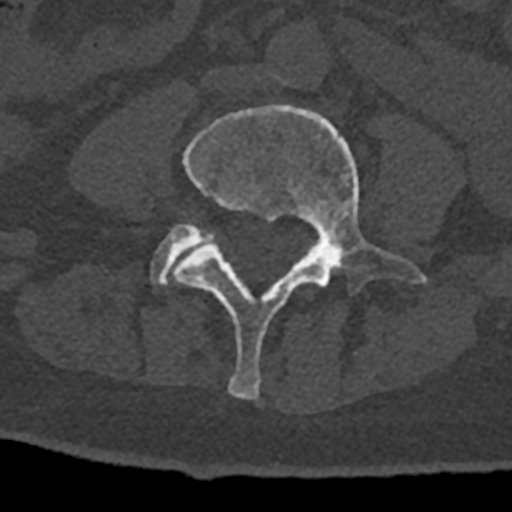
CT including the spine, one axial slice; slice 250 of 797 in the series (ordered by position); reconstruction kernel Br40s/3; bone window (W 1800 / L 400 HU); 0.5 mm slice thickness; 512 × 512 image matrix. Male patient, age 74 years. From the clinical record (not read from this slice): primary cancer: renal; vertebrae with lytic lesions (as recorded): T10, L1, L2, L3, L4, L5.
Structures marked on this image (semi-automatically segmented with operator editing):
- L4 vertebra: bounding box [x1, y1, x2, y2] px = [173, 105, 427, 400]
- L5 vertebra: [151, 224, 213, 285]